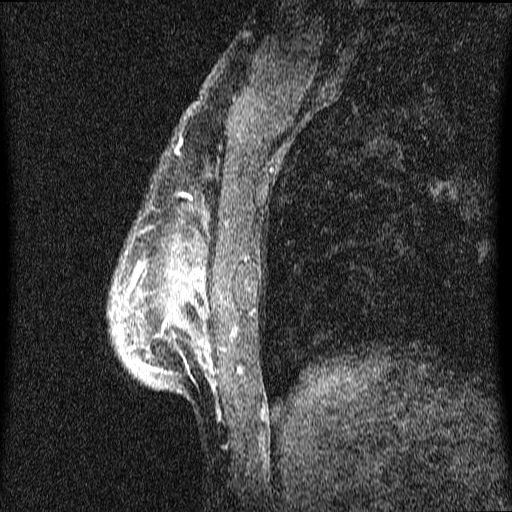
Breast MRI (dynamic contrast-enhanced), one sagittal slice; slice 15 of 64 in the series (ordered by position); dynamic contrast-enhanced series, image 2 of 4 at this slice position (ordered by acquisition); 1.5 T; TE 4.2 ms, TR 9.1 ms; 2 mm slice thickness; 512 × 512 image matrix. Patient: female, 33 years.
Outlined on this slice (semi-automatic segmentation, software-assisted and operator-edited):
- analysis volume of interest (the breast-tissue region the enhancement analysis was run in; not a lesion): box from (x=110, y=162) to (x=259, y=420) px
- tumour enhancement mask (voxels above the 70 % enhancement threshold inside the analysis volume of interest): (x=128, y=198)–(x=215, y=374)